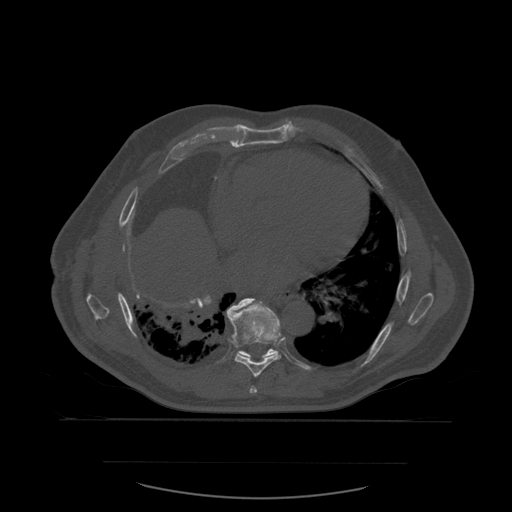
CT including the spine, one axial slice. Slice 356 of 590 in the series (ordered by position). Bone window (W 1800 / L 400 HU). 1.25 mm slice thickness. 512 × 512 image matrix, field of view 479 × 479 mm. Patient age 71 years. Case-level facts recorded for this patient, not image findings: primary cancer: lung; vertebrae with lytic lesions (as recorded): T1, T2, L5, S1.
Annotated regions visible in this slice (semi-automatic segmentation, software-assisted and operator-edited):
- T7 vertebra: bounding box [x1, y1, x2, y2] px = [250, 386, 258, 394]
- T8 vertebra: [227, 299, 282, 378]
- T9 vertebra: [239, 299, 276, 358]